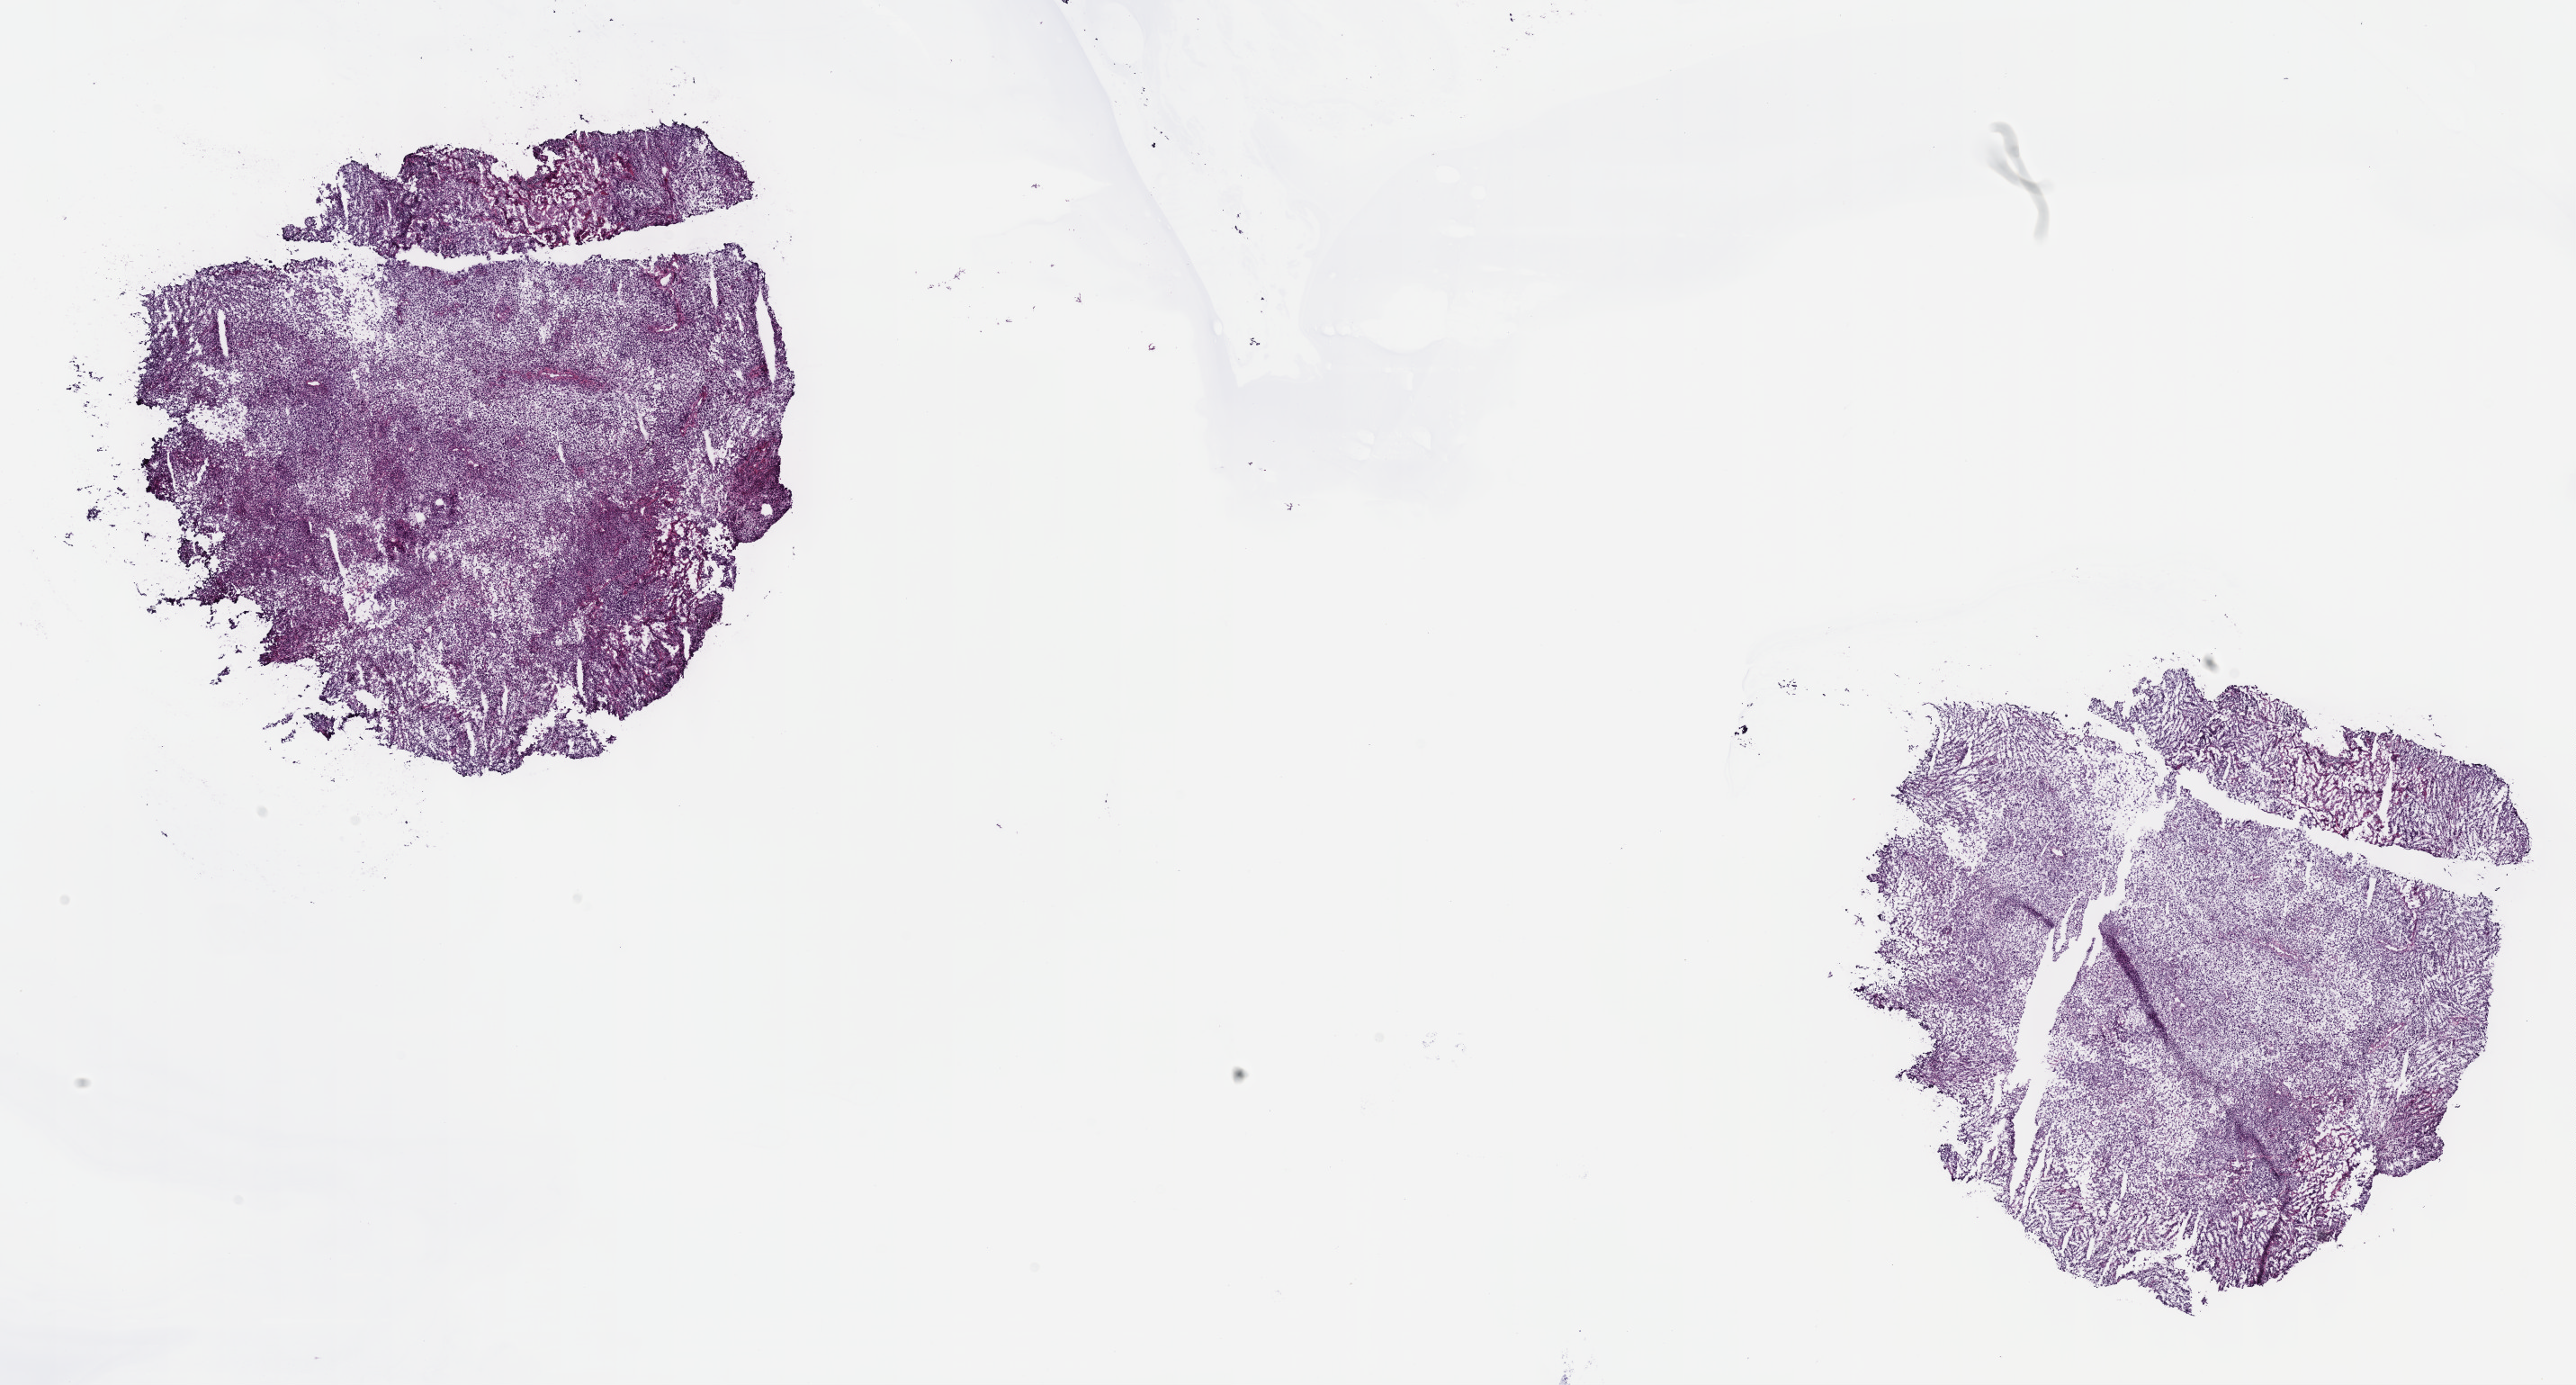
H&E whole-slide image — whole scanned area (about 23.2 x 12.4 mm) shown as a low-resolution overview; frozen section from the top of the tissue portion; metastatic tumour sample, sampled site: lower lobe, lung. Female, age 60 years at initial diagnosis. Pathologist review of this section (percent, as recorded): tumour cells 100%, tumour nuclei 80%, normal cells 0%, stromal cells 0%, necrosis 0%. Inflammatory infiltration, as recorded: lymphocyte infiltration 2%, monocyte infiltration 0%, neutrophil infiltration 0%.
* this section: metastatic tumour tissue
* patient diagnosis: Malignant melanoma, NOS